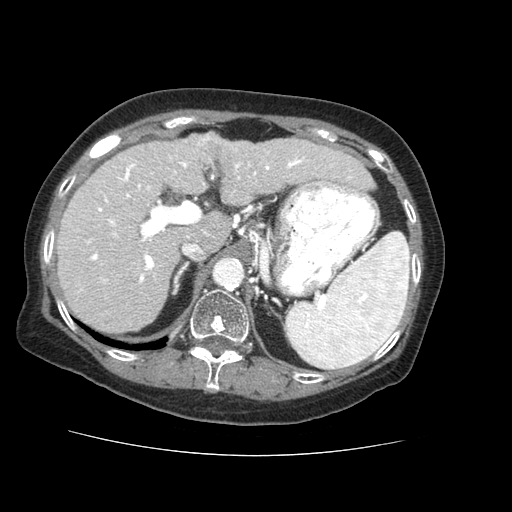
Contrast-enhanced abdominal CT (liver protocol), one axial slice. Position 40 of 73 along the scan axis. 120 kVp. Soft-tissue window (W 400 / L 40 HU). 2.5 mm slice thickness. 512 × 512 image matrix, field of view 360 × 360 mm. From the clinical record (not read from this slice): diagnosis: hepatocellular carcinoma (patient treated with transarterial chemoembolisation; whether this scan precedes or follows treatment is not stated here); TNM stage (as recorded): Stage-IVB.
Outlined on this slice (semi-automatically segmented with operator editing):
- liver parenchyma outside the tumour (the mass and vessels are separate outlines, so this box may not span the whole liver): bounding box (x1, y1, x2, y2) in pixels: (56, 132, 374, 332)
- mass: (193, 133, 236, 161)
- liver vessels: (81, 152, 352, 290)